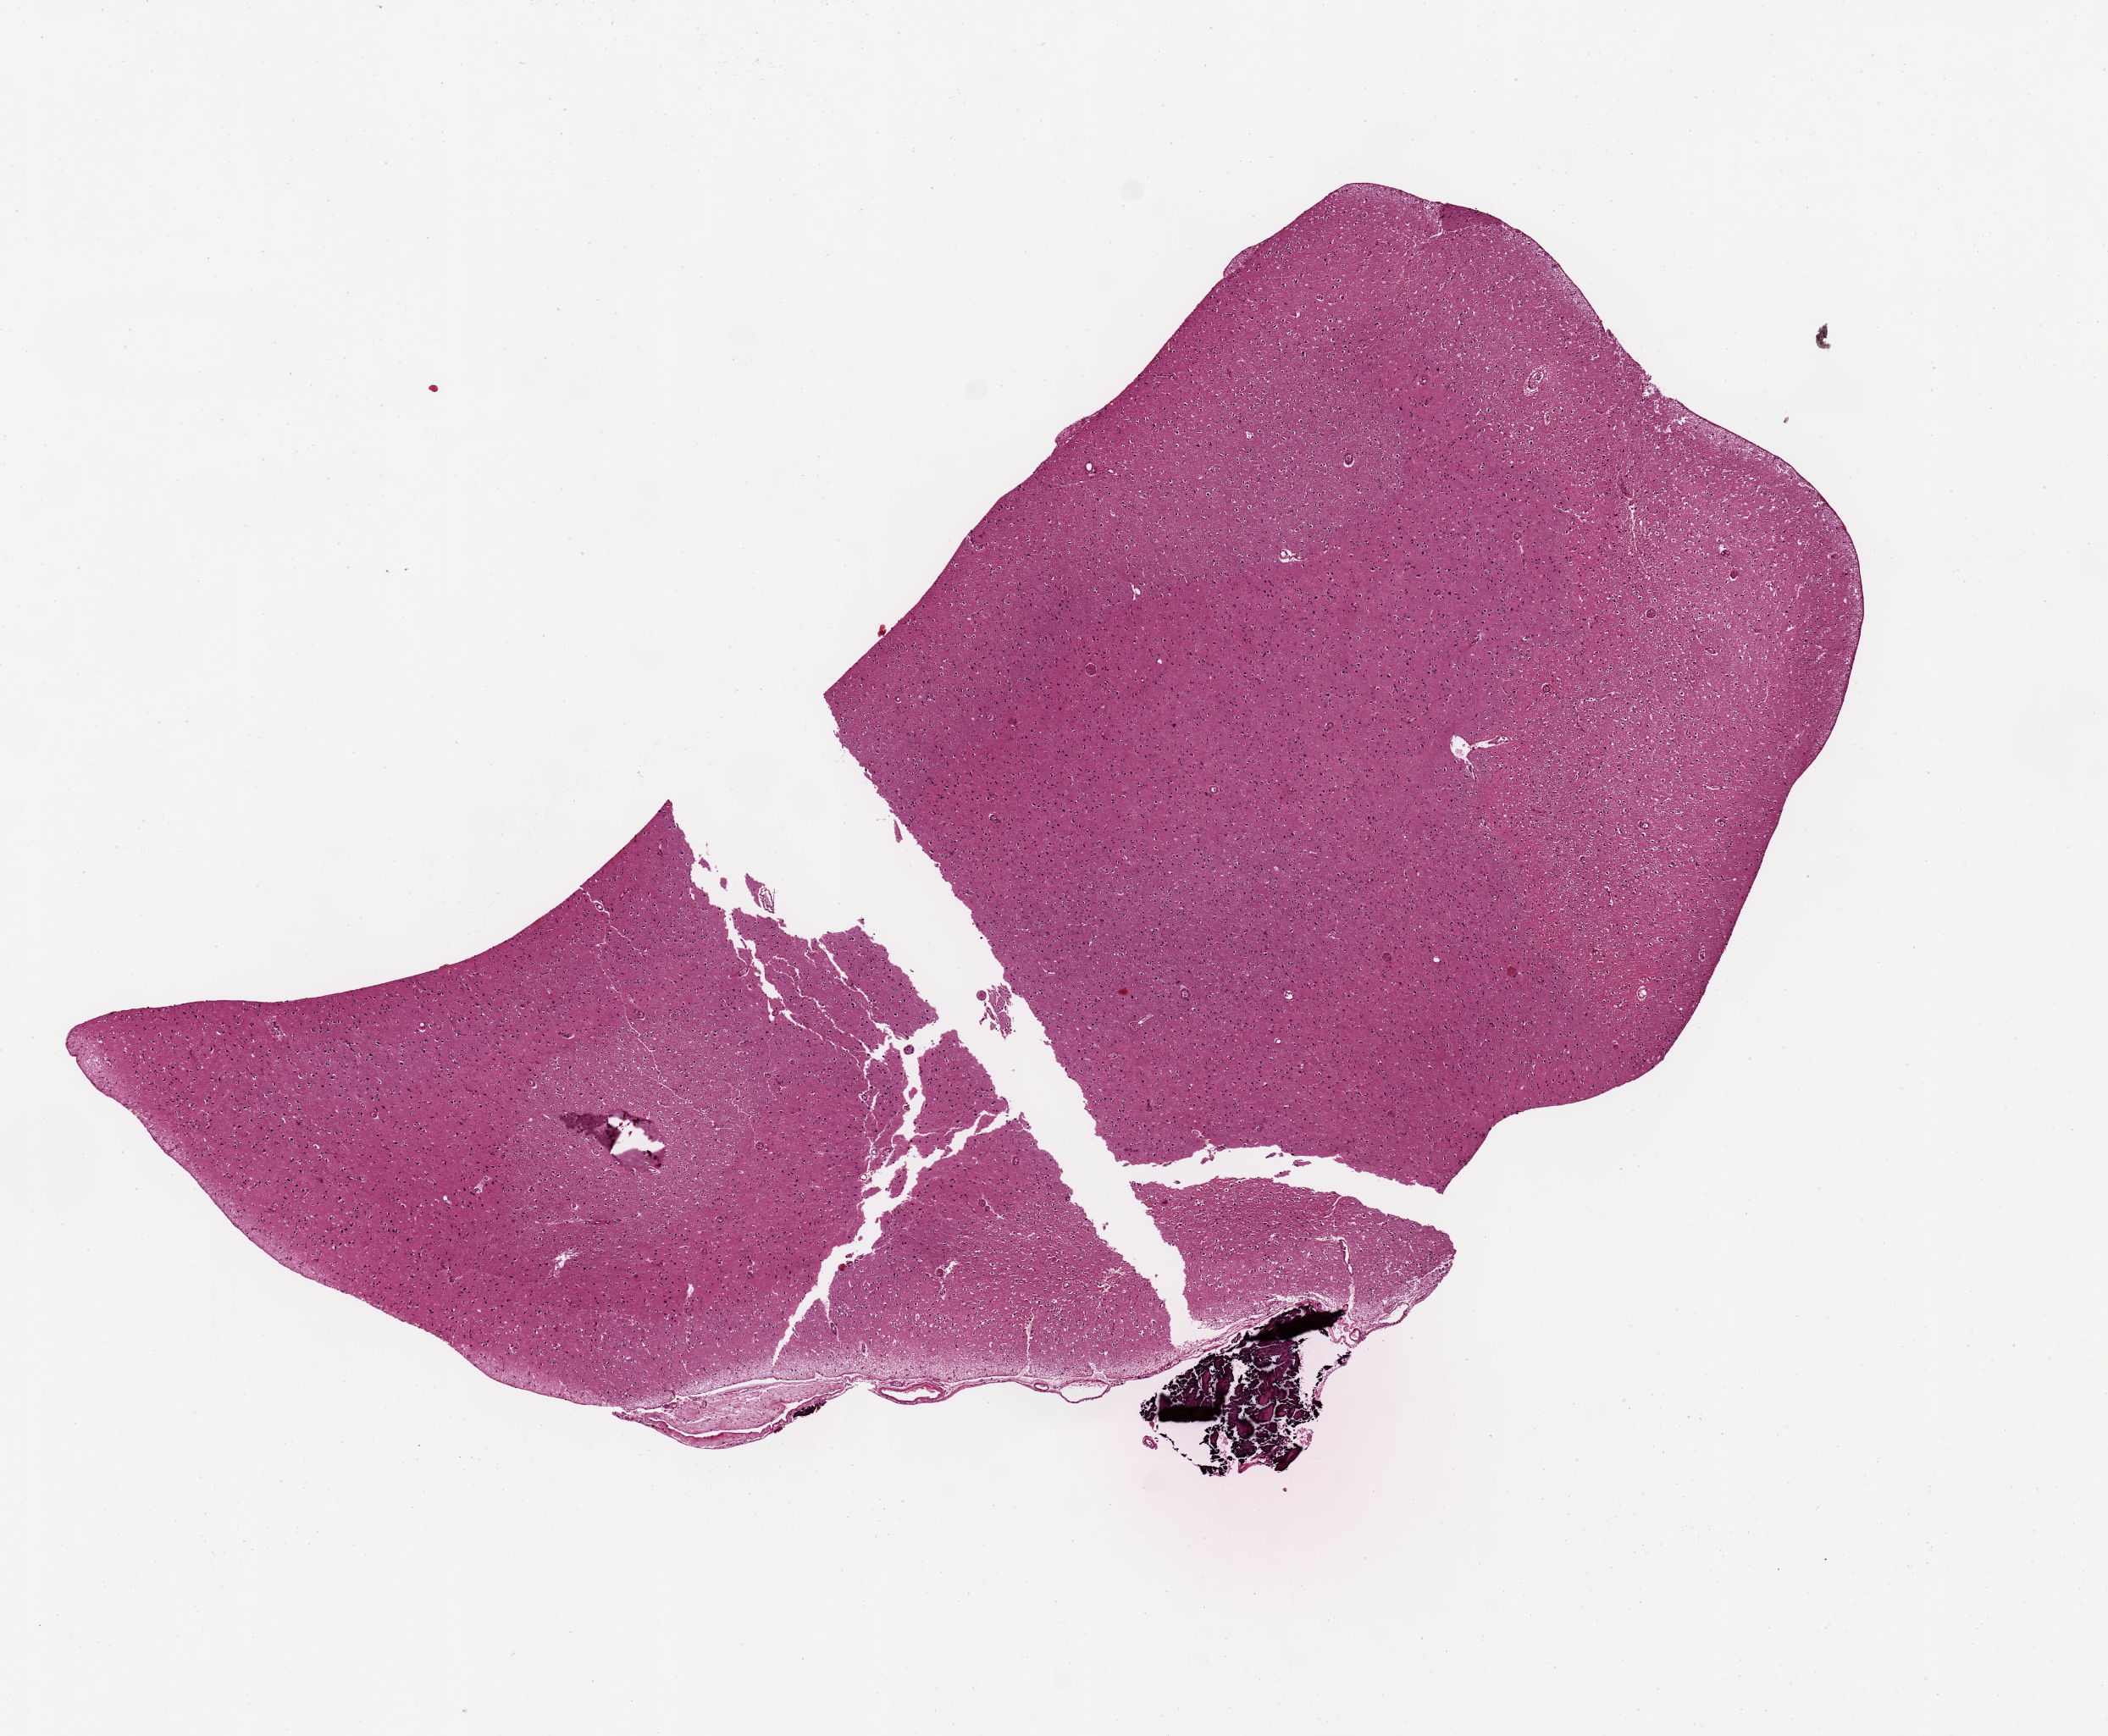
Digitized H&E-stained section, whole scanned area (about 9.8 x 8.1 mm, slide scanned at 20x) shown as a low-resolution overview, PAXgene-fixed, paraffin-embedded tissue, section of cerebral cortex (target tissue), donor tissue sample. Male donor.
Review note (as recorded): Not cerebellum but cortex.